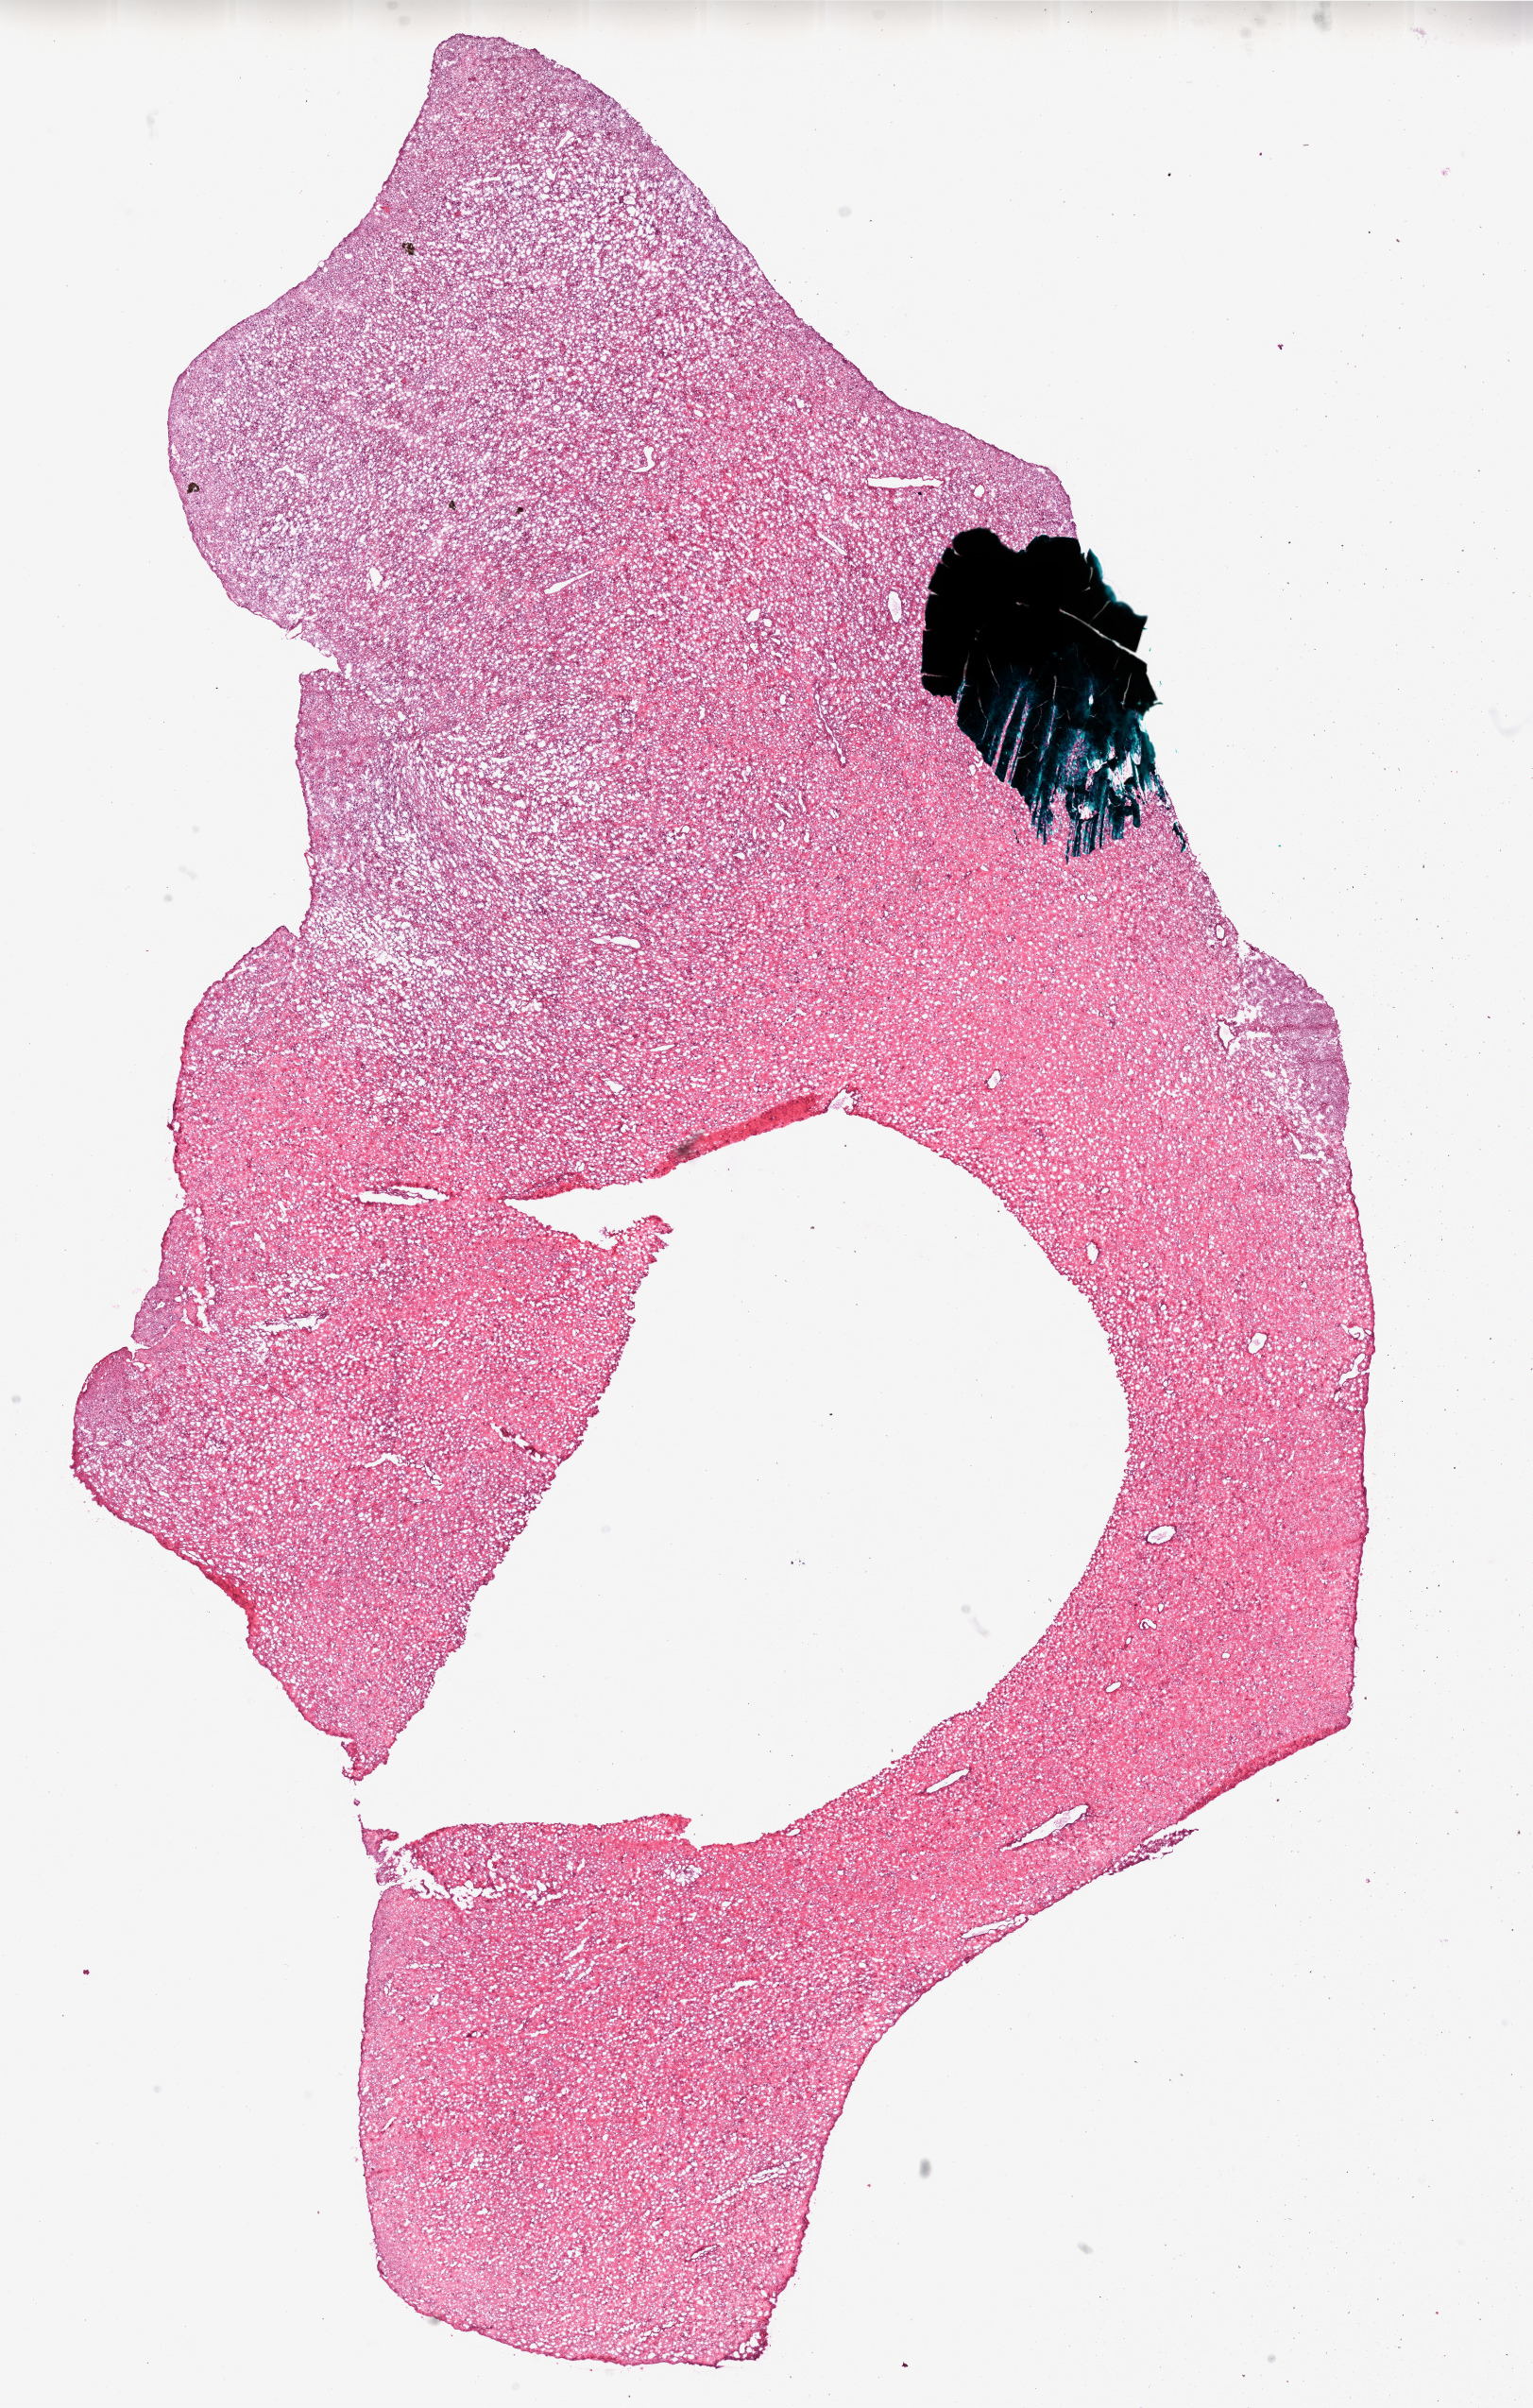
Hematoxylin and eosin (H&E) stained whole-slide image, whole scanned area (about 13.0 x 20.4 mm, slide scanned at 20x) shown as a low-resolution overview. Pathologist review of this section (percent, as recorded): tumour cells 50%, tumour nuclei 100%, stromal cells 50%, necrosis 0%.
Specimen: frozen section from the bottom of the tissue portion; sample: primary tumour, brain.